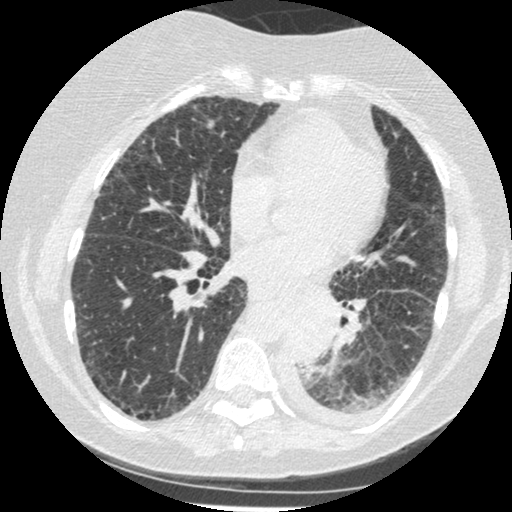
Low-dose screening chest CT, one axial slice; slice 100 of 341 in the series (ordered by position); reconstruction kernel STANDARD; 120 kVp; lung window (W 1500 / L -600 HU); 512 × 512 image matrix, field of view 310 × 310 mm.
Annotated regions visible in this slice (outlined manually by an expert reader):
- lesion 1 (tumor, lower lobe of left lung): bounding box (x1, y1, x2, y2) in pixels: (286, 307, 337, 363)